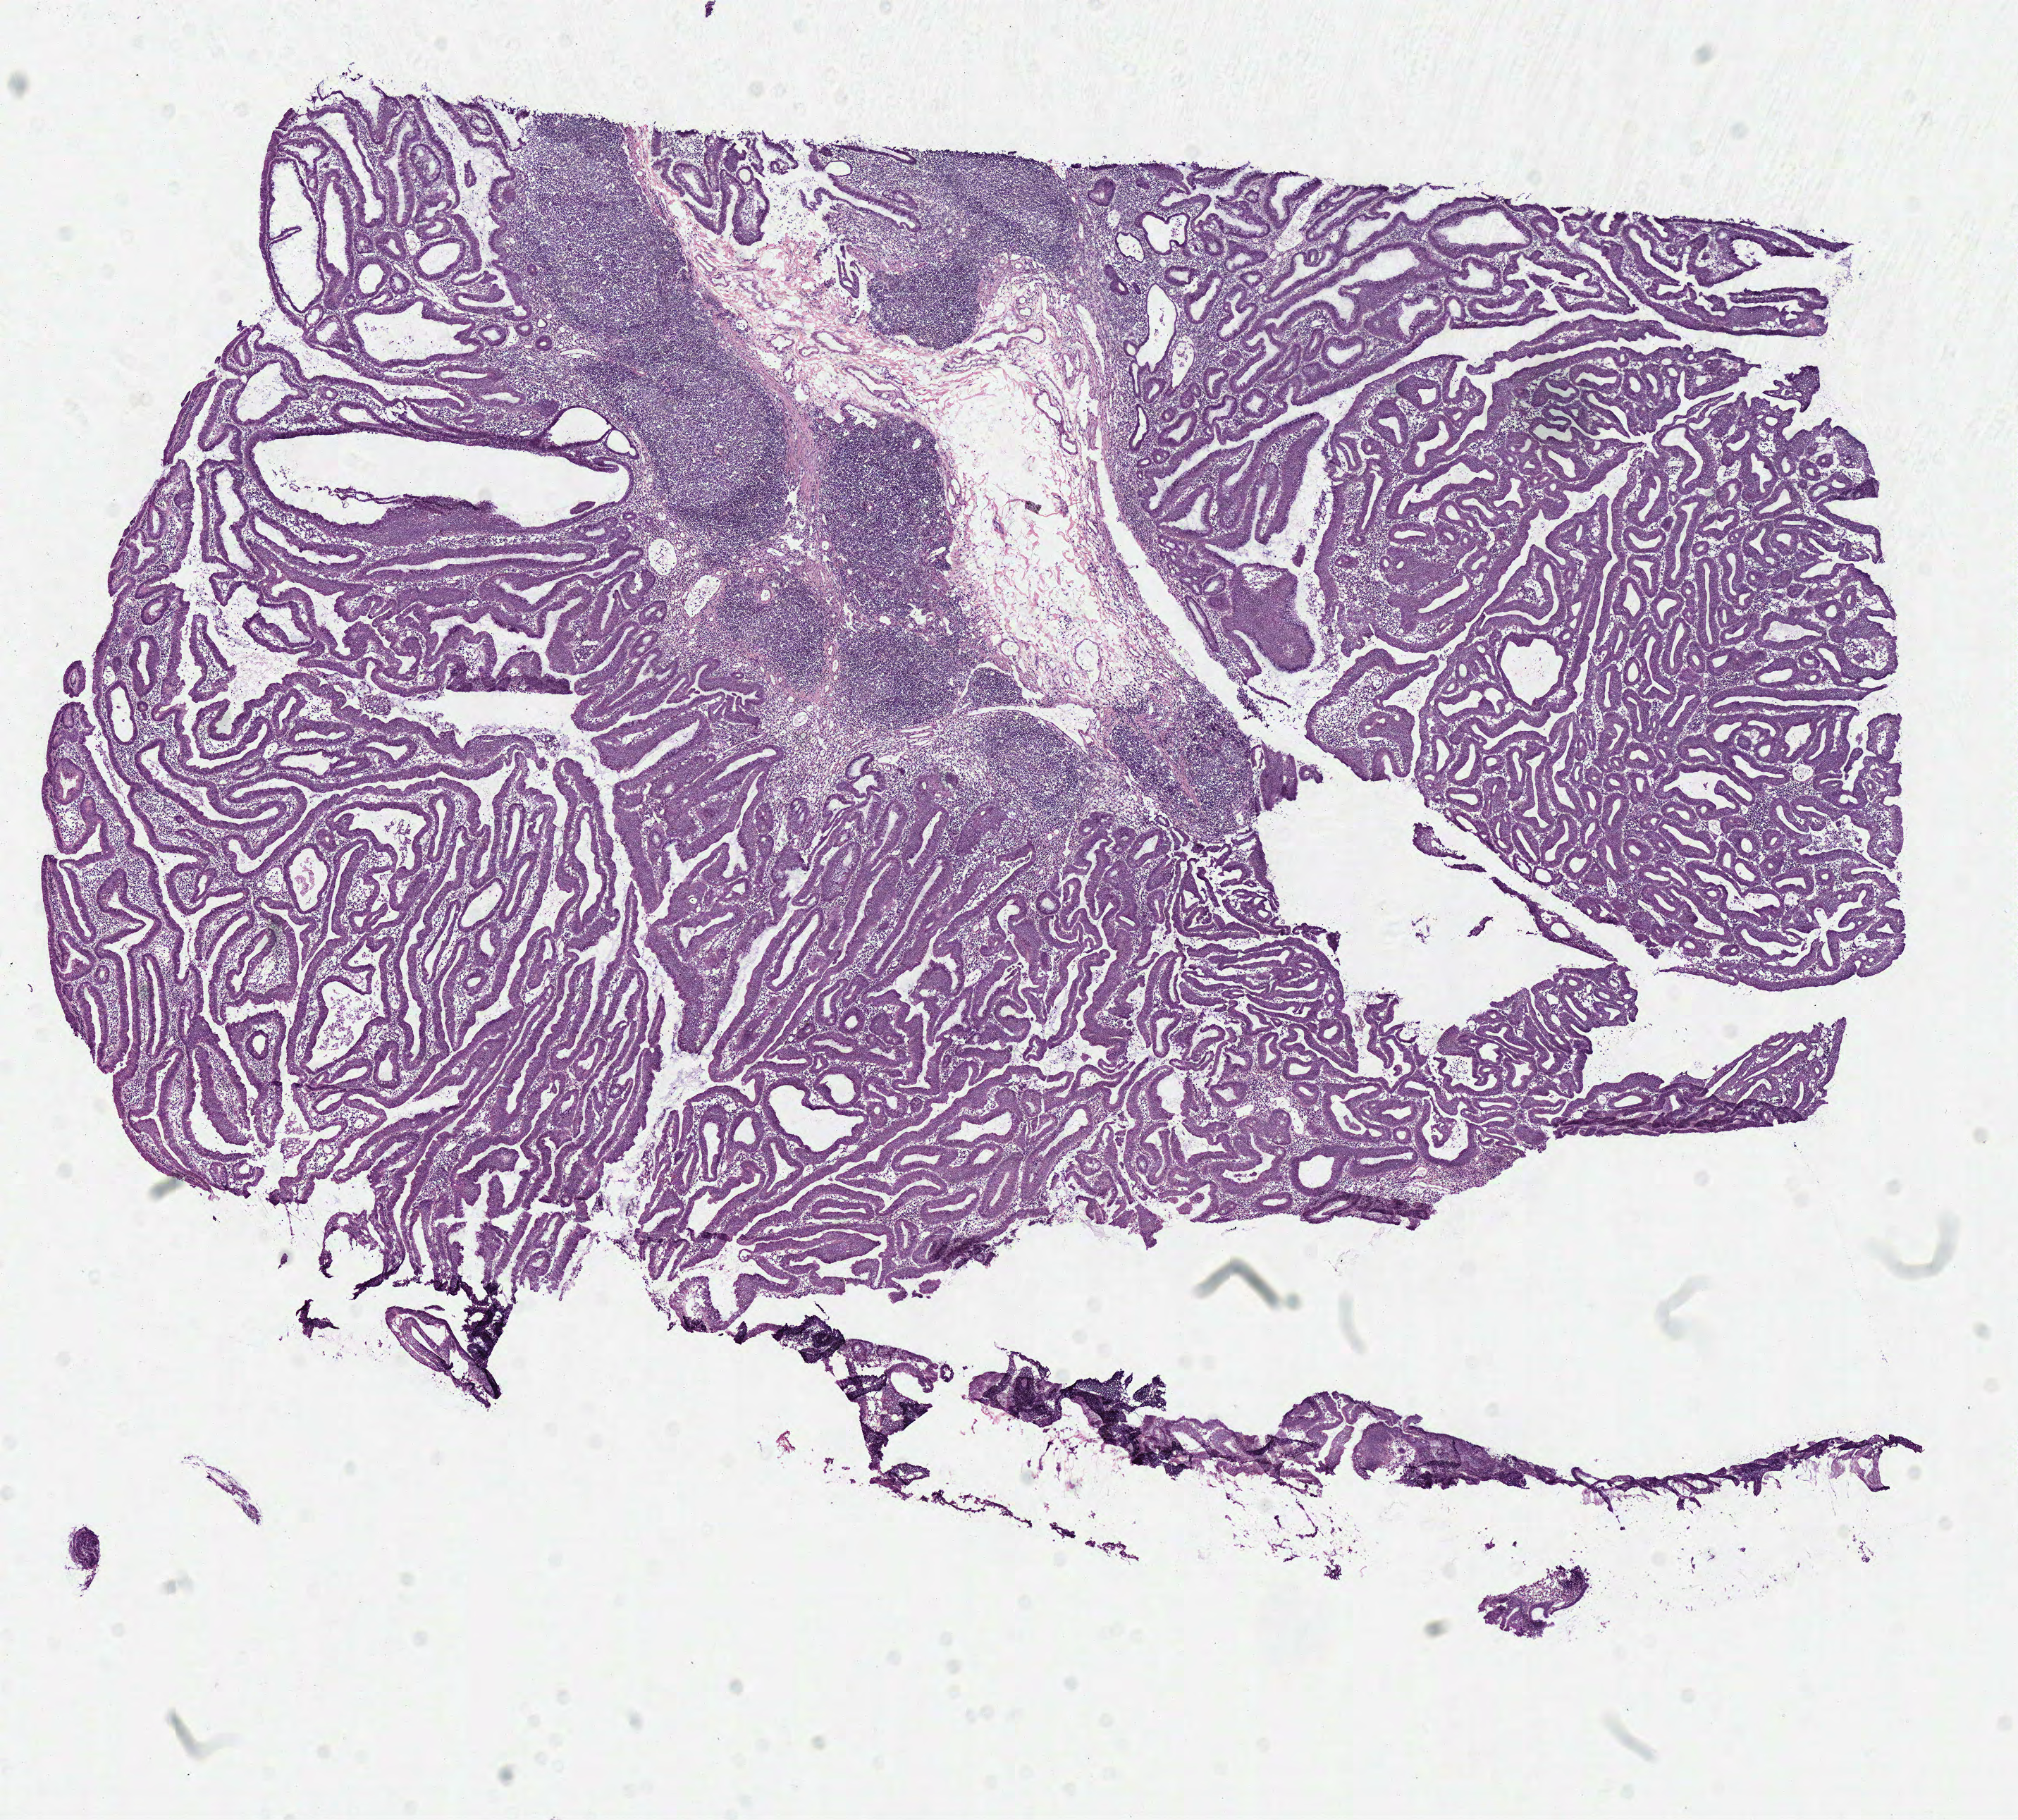
Digitized Hematoxylin and eosin (H&E) stained tissue section (whole slide) — shown as a low-resolution overview of the whole scanned area (about 11.3 x 10.2 mm). Frozen section. Colon, primary tumour sample. Male, age 50 years at initial diagnosis. Composition of this section per pathologist review: tumour cells 90%, tumour nuclei 70%, normal cells 0%, stromal cells 10%, necrosis 0%.
Histologic diagnosis: Adenocarcinoma, NOS (cecum). AJCC pathologic stage: IA.